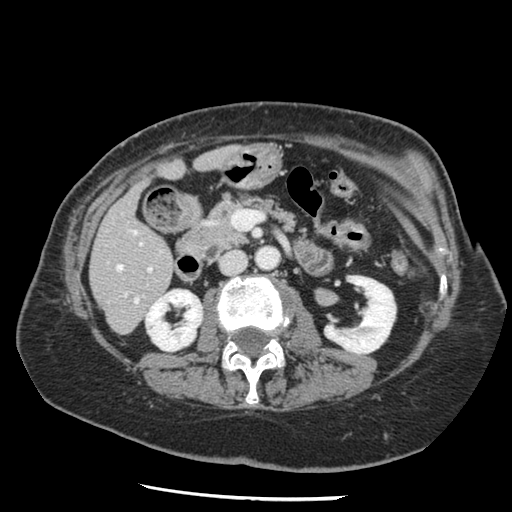
Contrast-enhanced abdominal CT, one axial slice. Slice 53 of 148 in the series (ordered by position). Reconstruction kernel STANDARD. 120 kVp. Intravenous contrast given. Soft-tissue window (W 400 / L 40 HU). 2.5 mm slice thickness. 512 × 512 image matrix, field of view 330 × 330 mm. Female patient, age 85 years. From the clinical record (not read from this slice): diagnosis: colorectal cancer liver metastases, imaged before liver resection; multiple liver metastases: no; largest metastasis: 0.9 cm; disease in both lobes: no.
Annotated regions visible in this slice (manually delineated by an expert):
- hepatic veins: bounding box (x1, y1, x2, y2) in pixels: (116, 231, 138, 302)
- liver: (91, 148, 234, 333)
- planned liver remnant (the part of the liver to remain after resection): (91, 148, 234, 326)